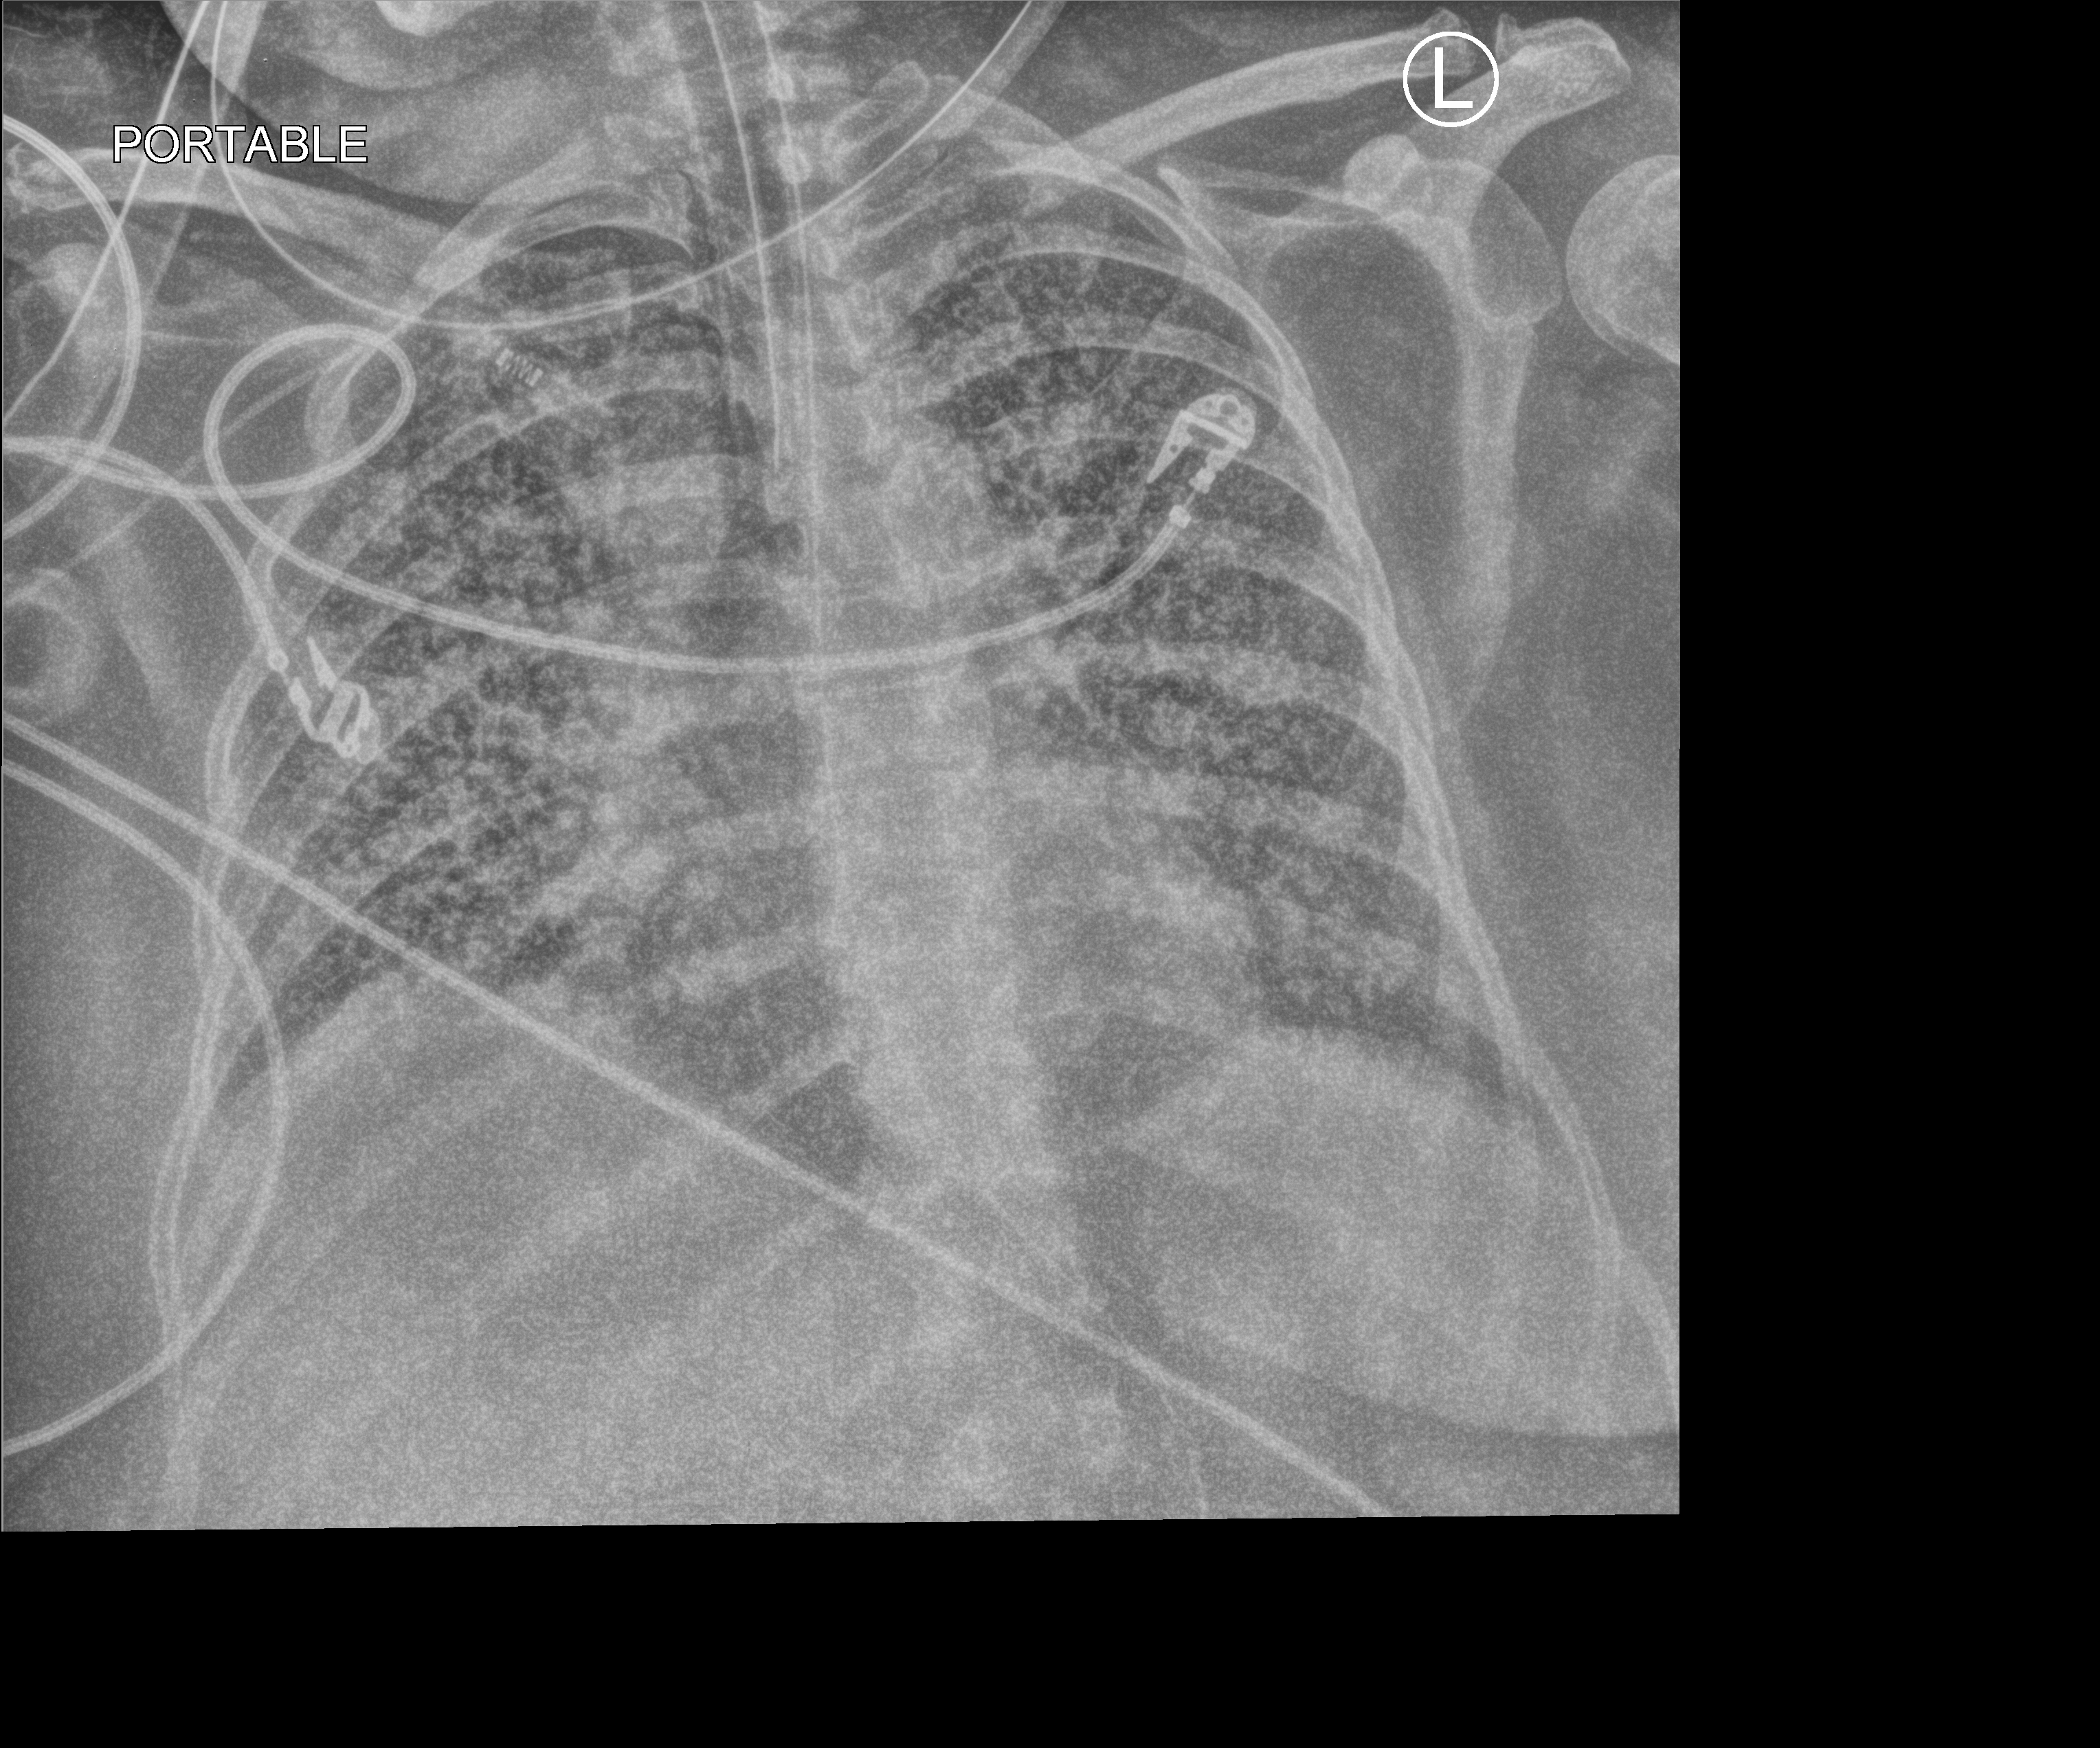
Chest X-ray (portable); anteroposterior (AP) projection. Female patient hospitalised with COVID-19, age 18–59 years.
From the hospital-stay record, not from the radiograph (when in the stay this image was taken is not recorded):
- admitted to intensive care during this hospital stay: yes
- mechanically ventilated during this hospital stay: yes
- length of hospital stay: 95 days